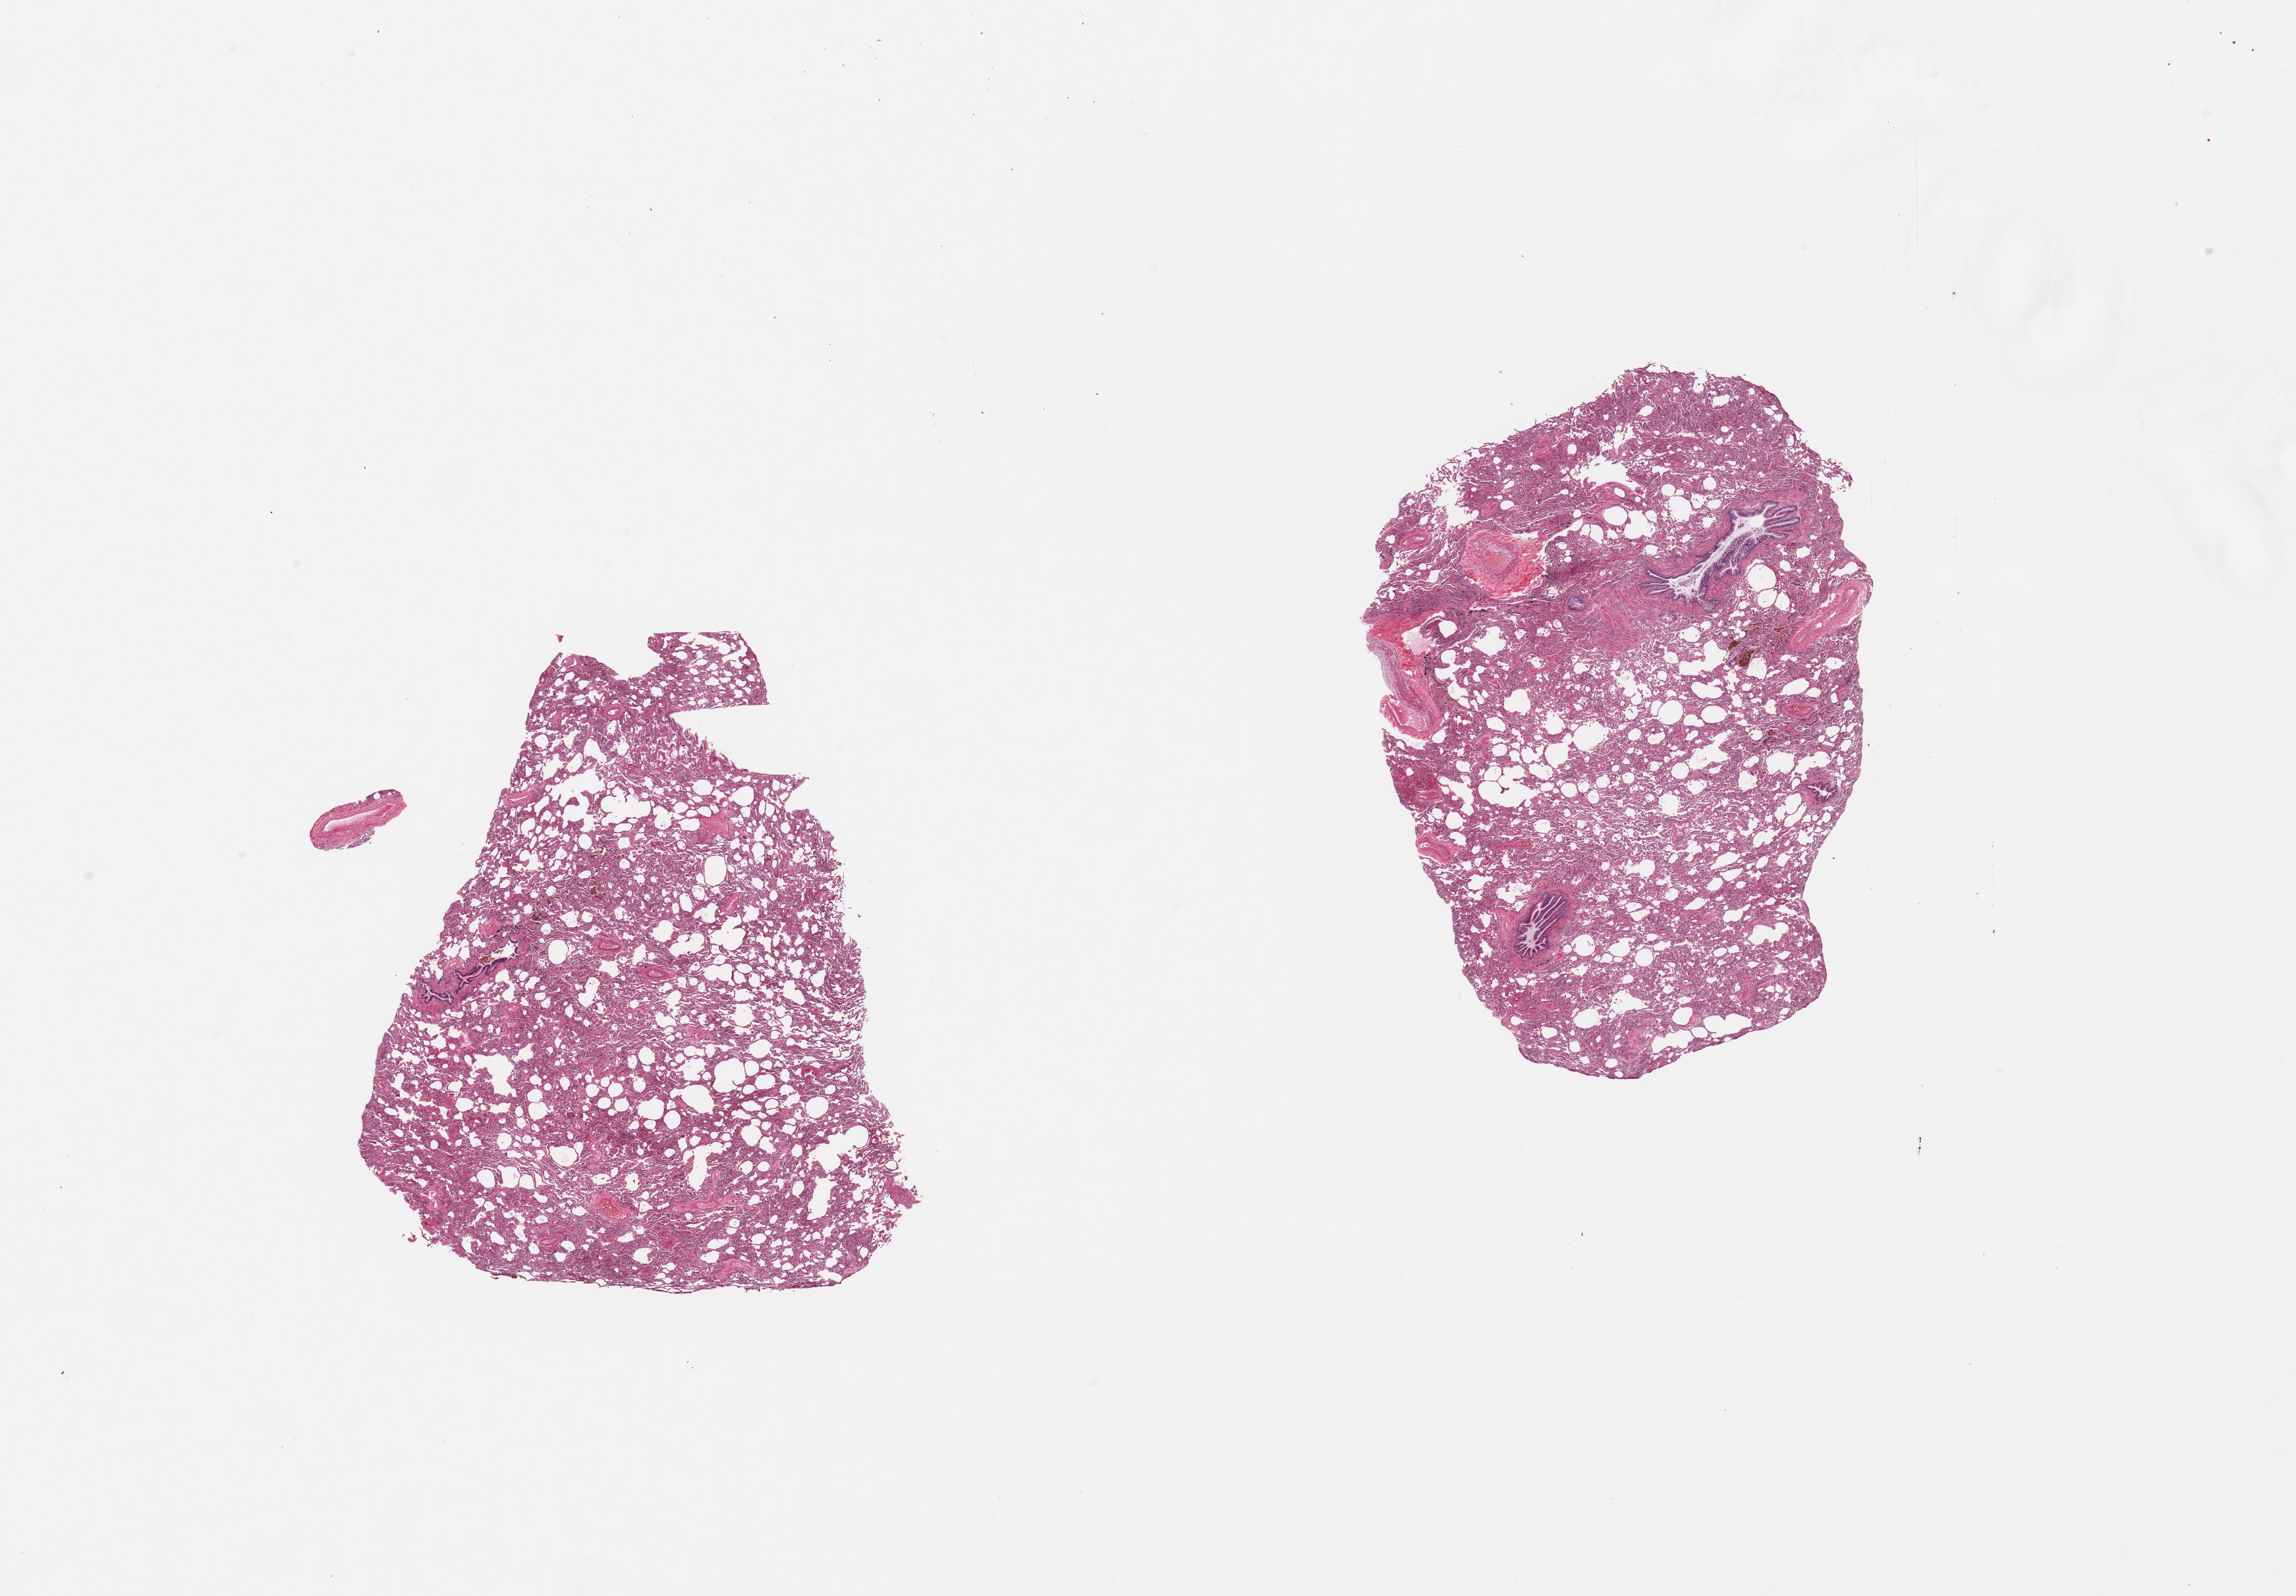
Haematoxylin and eosin whole-slide image, shown as a low-resolution overview of the whole scanned area (about 27.6 x 19.2 mm, acquisition: 20x scan). PAXgene-fixed, paraffin-embedded tissue. Sampled site (target tissue): lung. Tissue donor sample. Donor sex: female.
Reviewer comment on this tissue sample: 2 pieces; some collapse, pigmented macrophages.